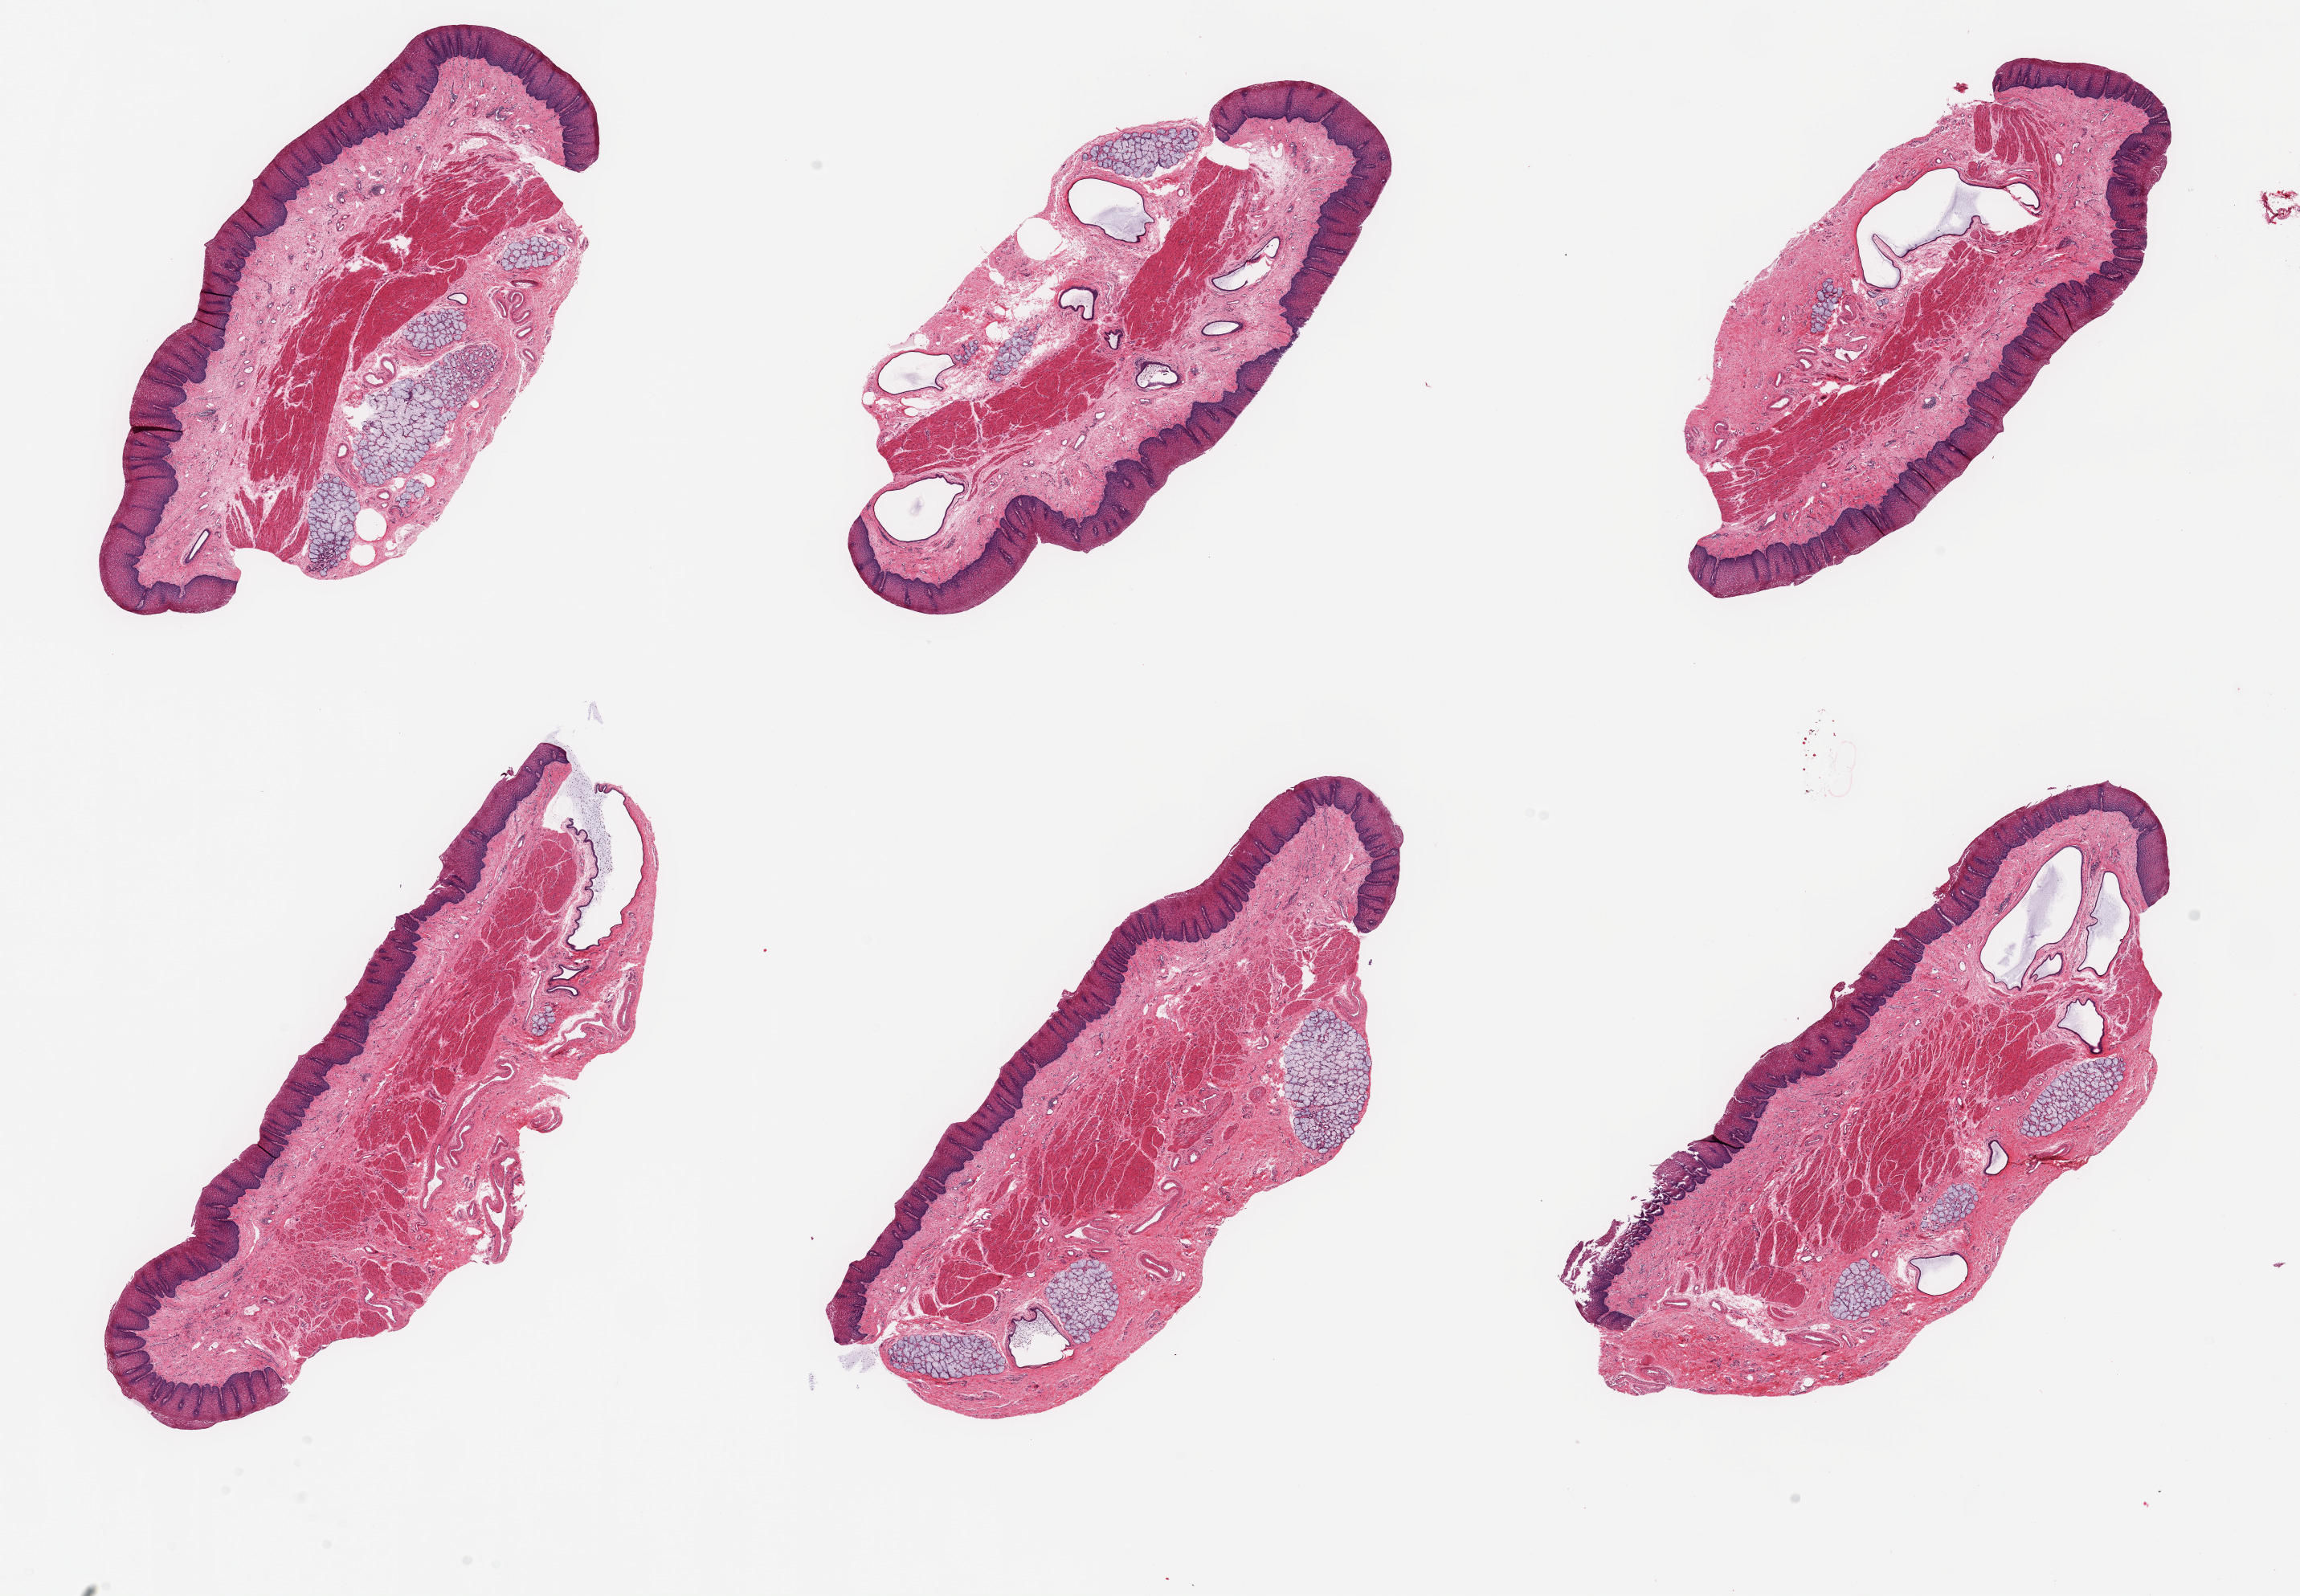
Whole-slide image, haematoxylin and eosin stain, brightfield — a low-resolution overview of the entire scanned area, about 22.6 x 15.7 mm (slide scanned at 20x); PAXgene-fixed, paraffin-embedded tissue; sampled site (target tissue): esophageal mucous membrane; tissue donor sample. Male donor.
Reviewer comment on this tissue sample: 6 pieces, squamous mucosa up to ~0.5mm, 10-15% thickness; Prominent submucosal mucus glands present.